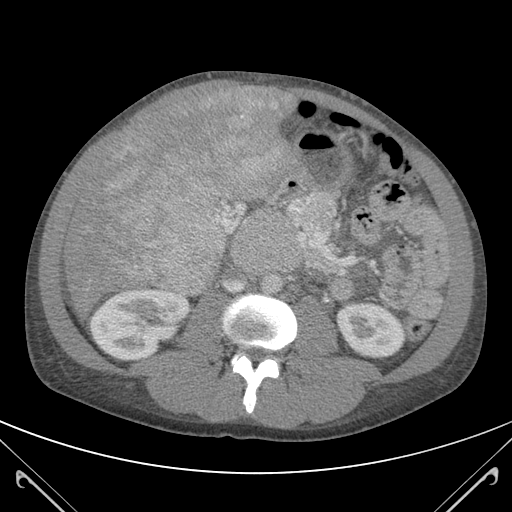
Contrast-enhanced abdominal CT (liver protocol), one axial slice; position 45 of 118 along the scan axis; 120 kVp; soft-tissue window (W 400 / L 40 HU); 3 mm slice thickness; 512 × 512 image matrix. Case-level facts recorded for this patient, not image findings: diagnosis: hepatocellular carcinoma (patient treated with transarterial chemoembolisation; whether this scan precedes or follows treatment is not stated here); TNM stage (as recorded): Stage-IIIB; Child-Pugh class: A; tumour nodularity: uninodular.
Outlined on this slice (semi-automatically segmented with operator editing):
- abdominal aorta: bounding box [x1, y1, x2, y2] px = [263, 274, 282, 296]
- liver parenchyma outside the tumour (the mass and vessels are separate outlines, so this box may not span the whole liver): [64, 87, 287, 312]
- mass: [94, 87, 293, 292]
- liver vessels: [273, 167, 275, 169]